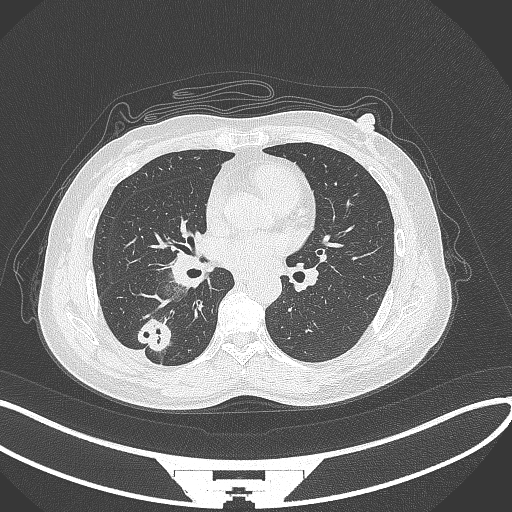
Chest CT, one axial slice. Slice 146 of 352 in the series (ordered by position). Reconstruction kernel B70f. Lung window (W 1500 / L -600 HU). 1 mm slice thickness. 512 × 512 image matrix, field of view 400 × 400 mm. Patient: female, 55 years. Case-level facts recorded for this patient, not image findings: clinical TNM (as recorded): T1c N1 M0.
Structures marked on this image (bounding box drawn by a radiologist):
- lung tumour (recorded histology: adenocarcinoma): bounding box <129,317,173,353> (left, top, right, bottom; pixels)